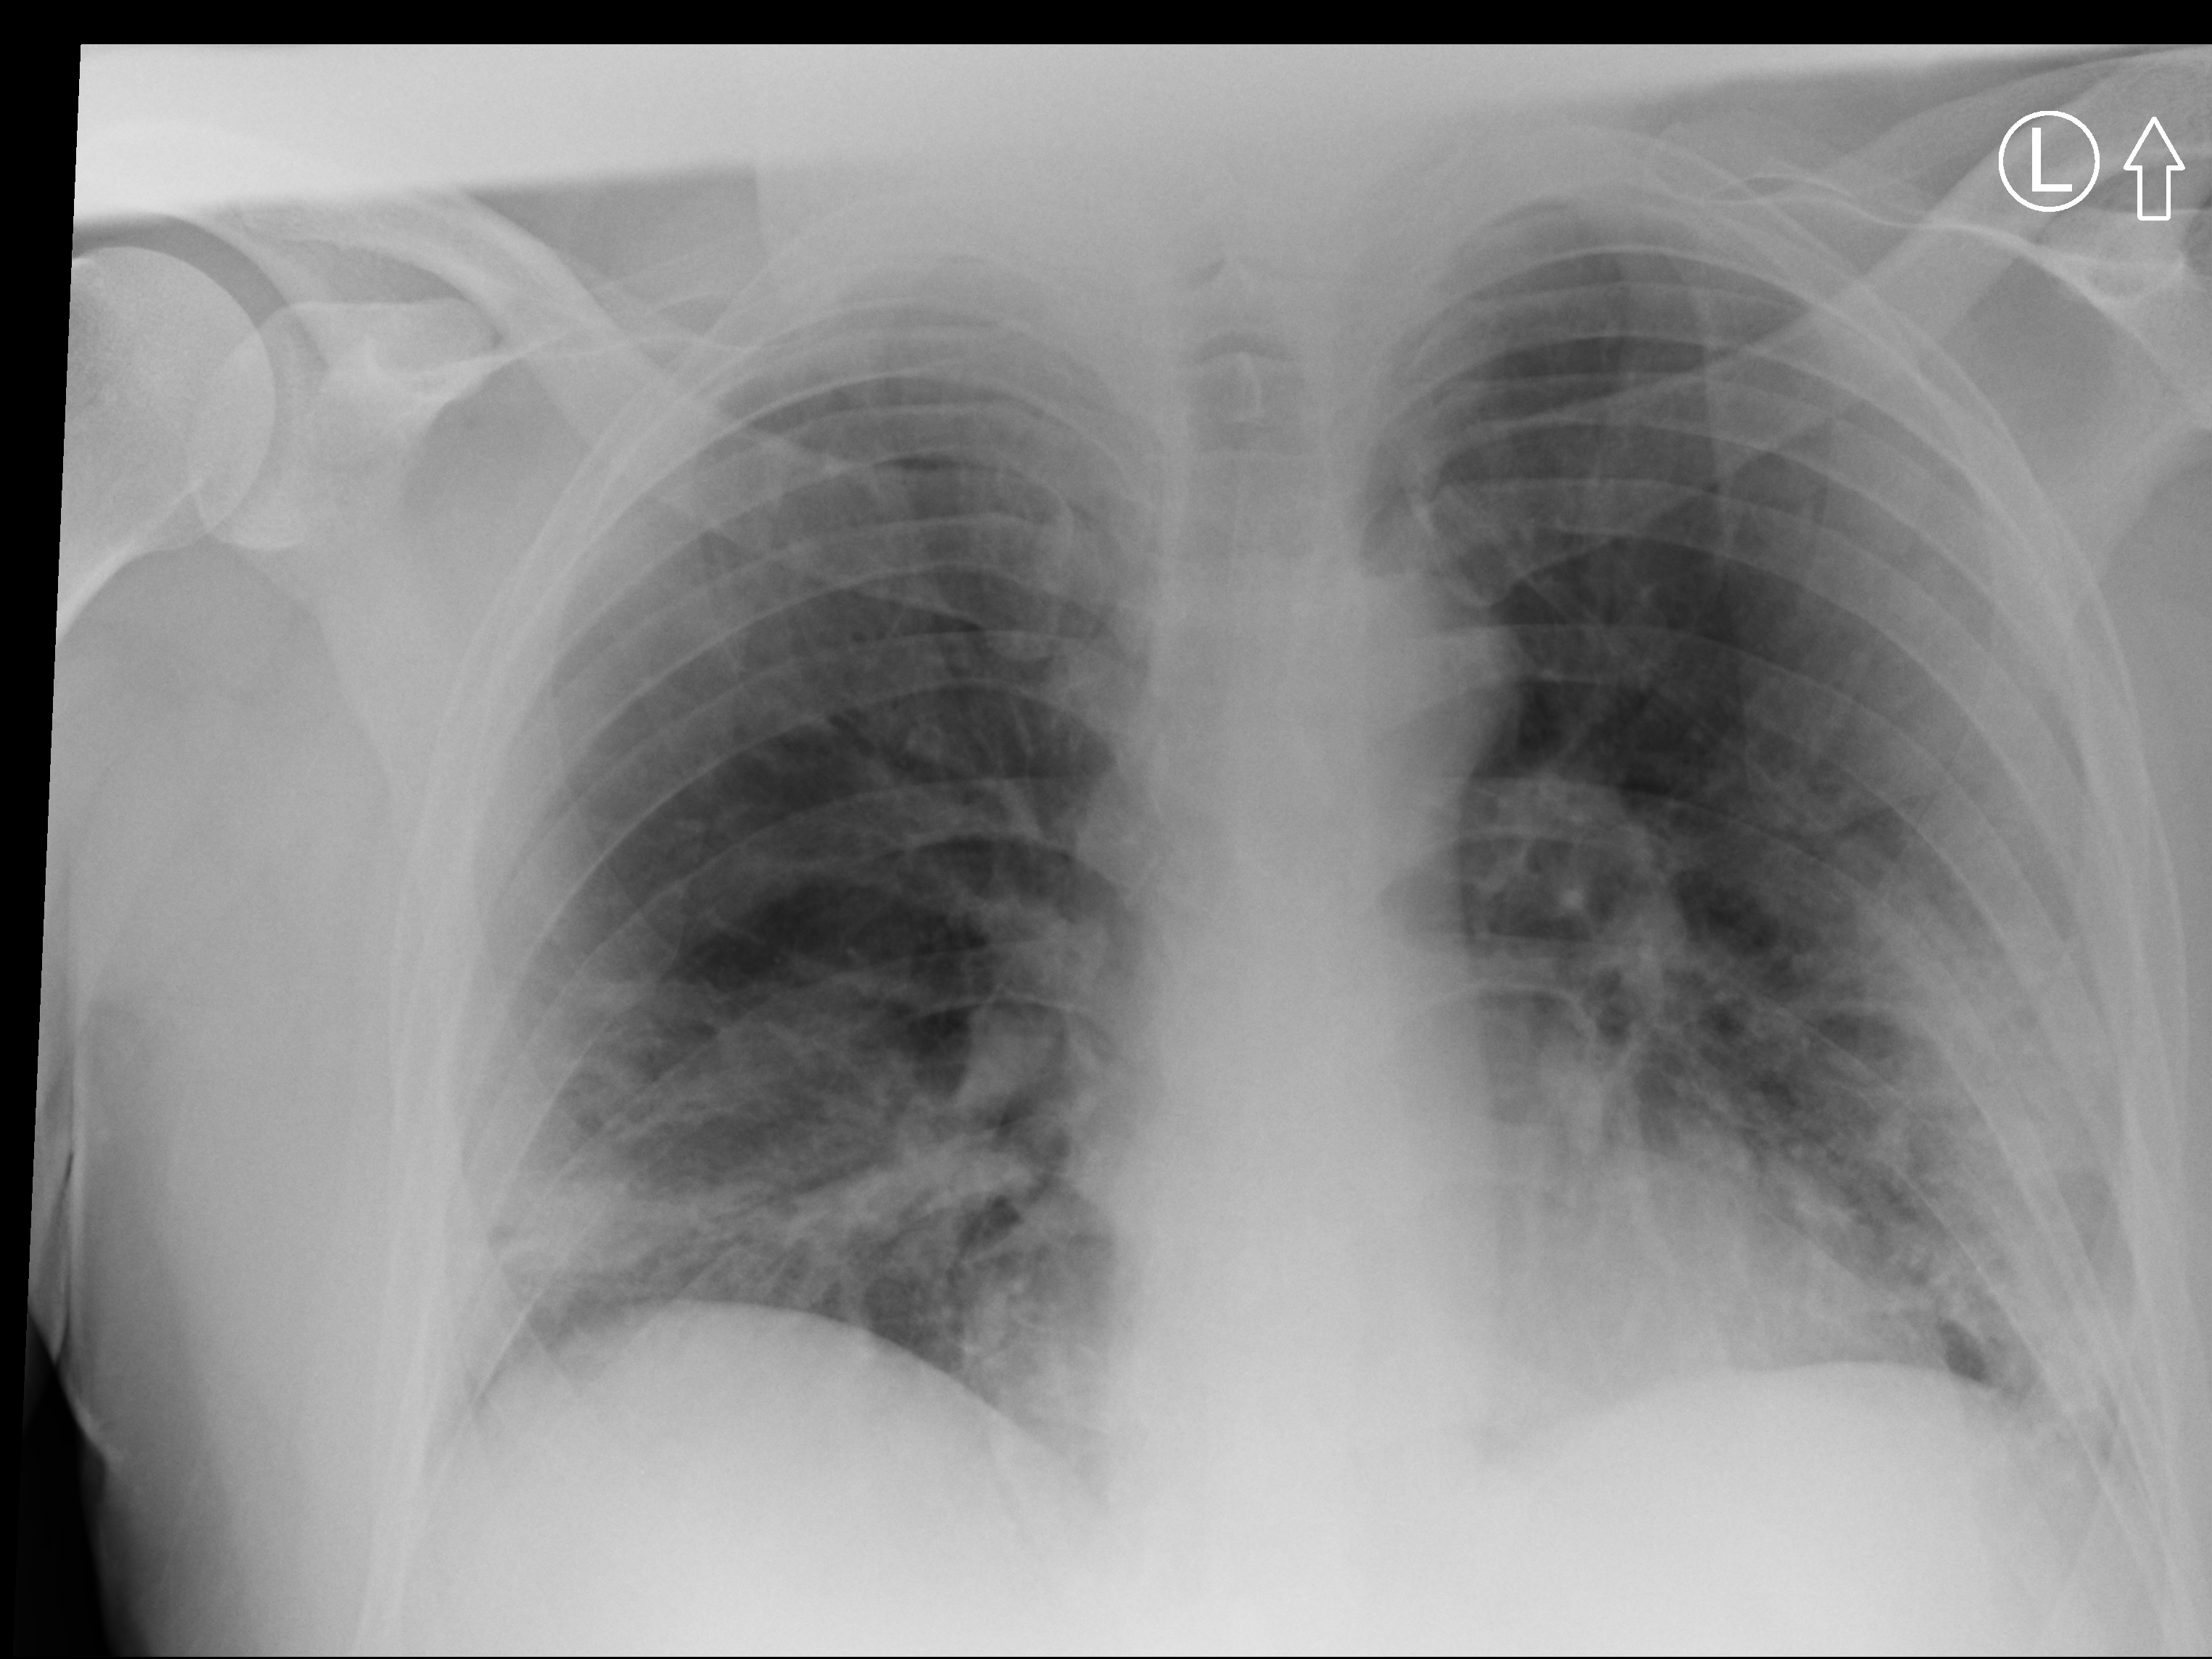
Portable chest radiograph; anteroposterior (AP) projection. Patient hospitalised with COVID-19; male, aged 18–59 years.
Admission-level facts for this patient (not findings on this image; timing relative to this image not recorded): smoking status (admission record): never; mechanically ventilated during this hospital stay: no.